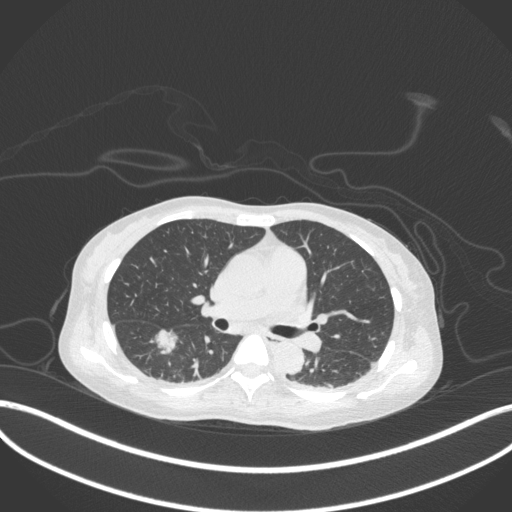
Chest CT, one axial slice. Position 177 of 260 along the scan axis. Reconstruction kernel B31f. Lung window (W 1500 / L -600 HU). 512 × 512 image matrix, field of view 400 × 400 mm. Female patient, age 44 years. Case-level facts recorded for this patient, not image findings: clinical TNM (as recorded): T1c N0 M0.
Outlined on this slice (rectangle marked by the reading radiologist):
- lung tumour (recorded histology: adenocarcinoma): box from (x=148, y=324) to (x=180, y=357) px